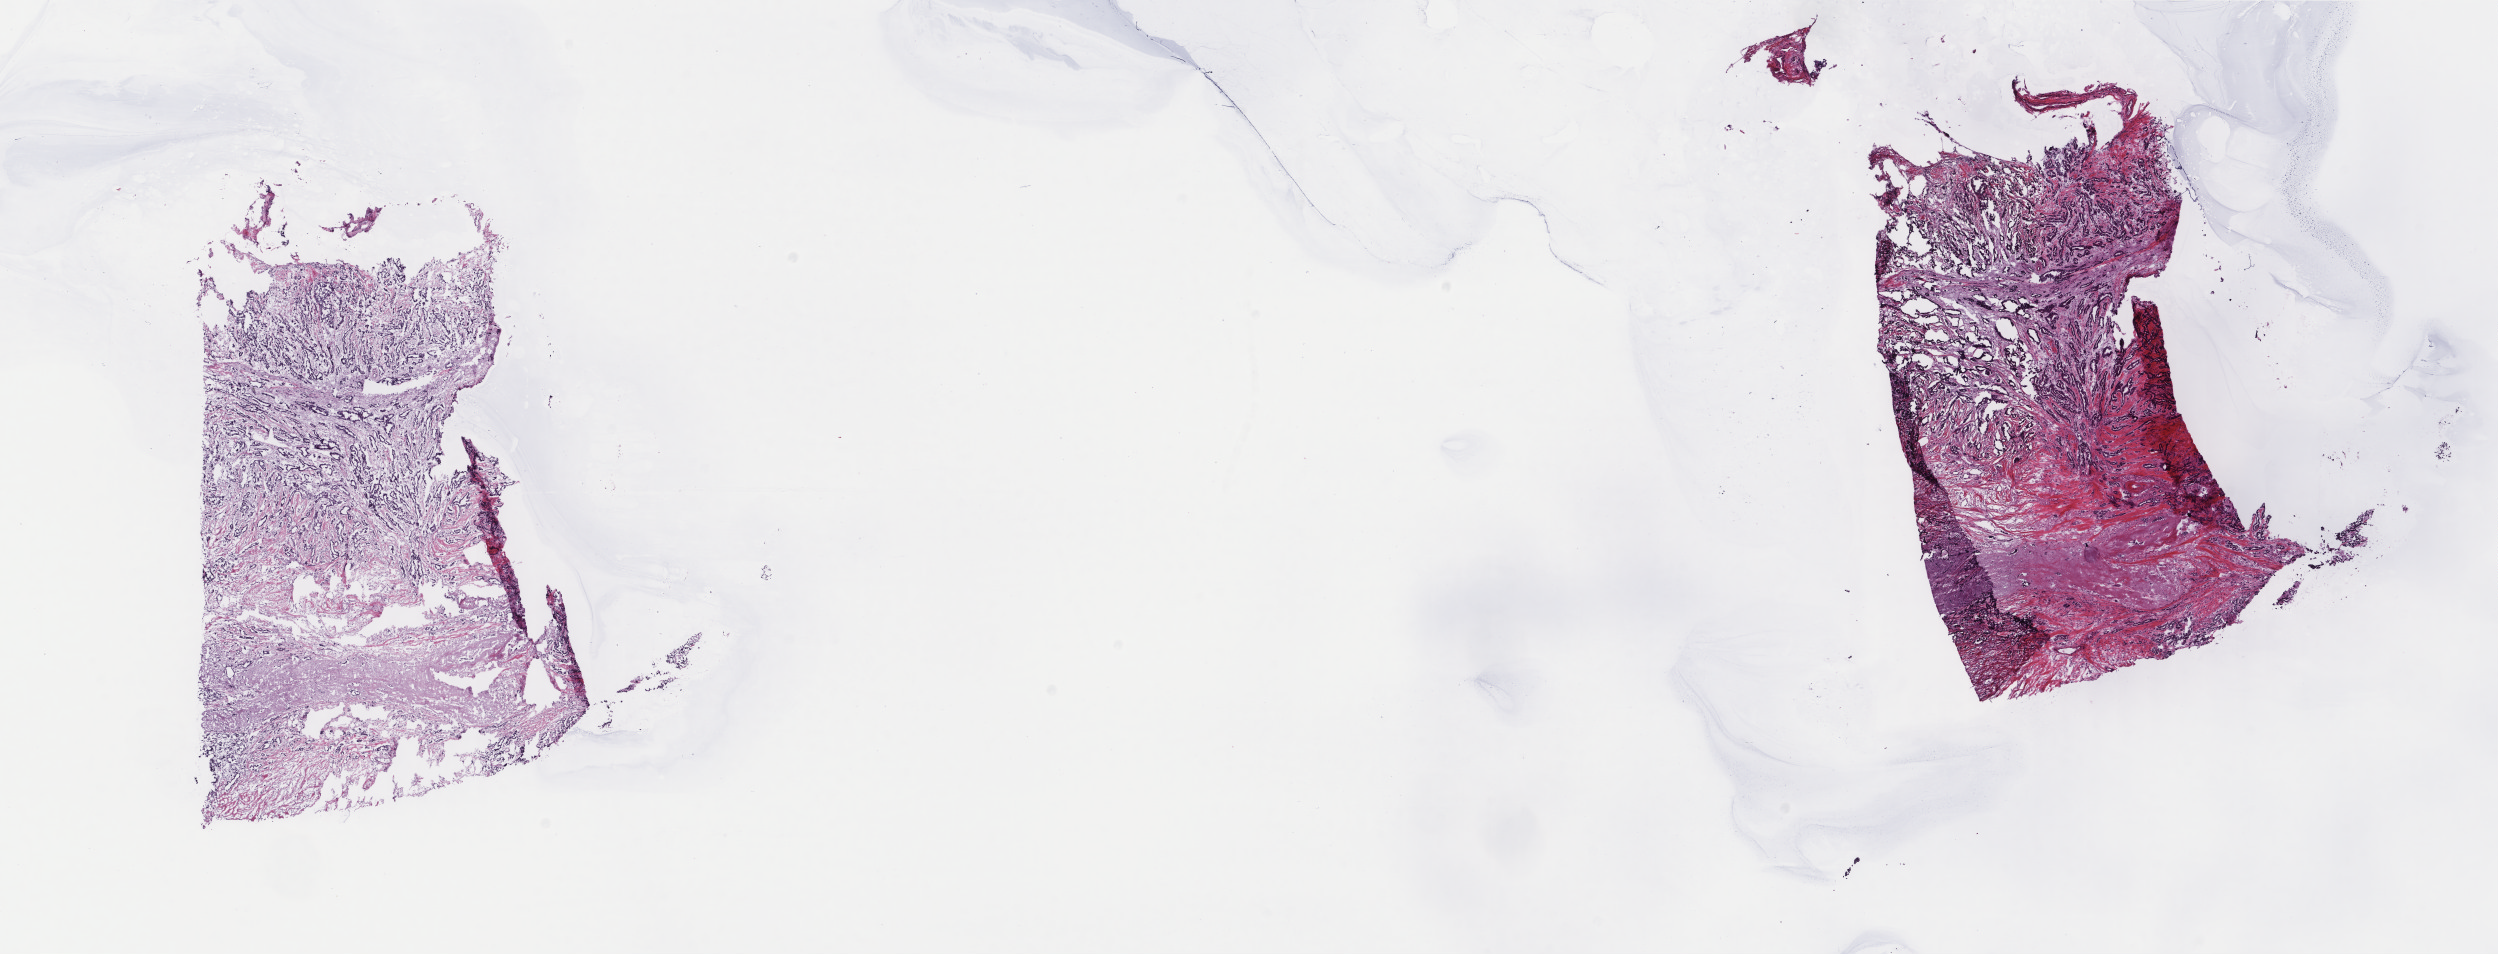
Digitized H&E tissue section (whole slide), low-resolution overview of the scanned area, about 19.8 x 7.6 mm (slide scanned at 40x); frozen section; breast, primary tumour sample. Female, age 77 years at initial diagnosis. Pathologist review of this section (percent, as recorded): tumour cells 70%, tumour nuclei 80%, normal cells 0%, stromal cells 30%, necrosis 0%. Inflammatory infiltration, as recorded: lymphocyte infiltration 0%, monocyte infiltration 0%, neutrophil infiltration 0%.
Histologic diagnosis: Infiltrating duct carcinoma, NOS. Lymph nodes positive (case pathology): 0 of 9 examined. TNM: T1 N1 M0. AJCC pathologic stage: IIA. Laterality: left.